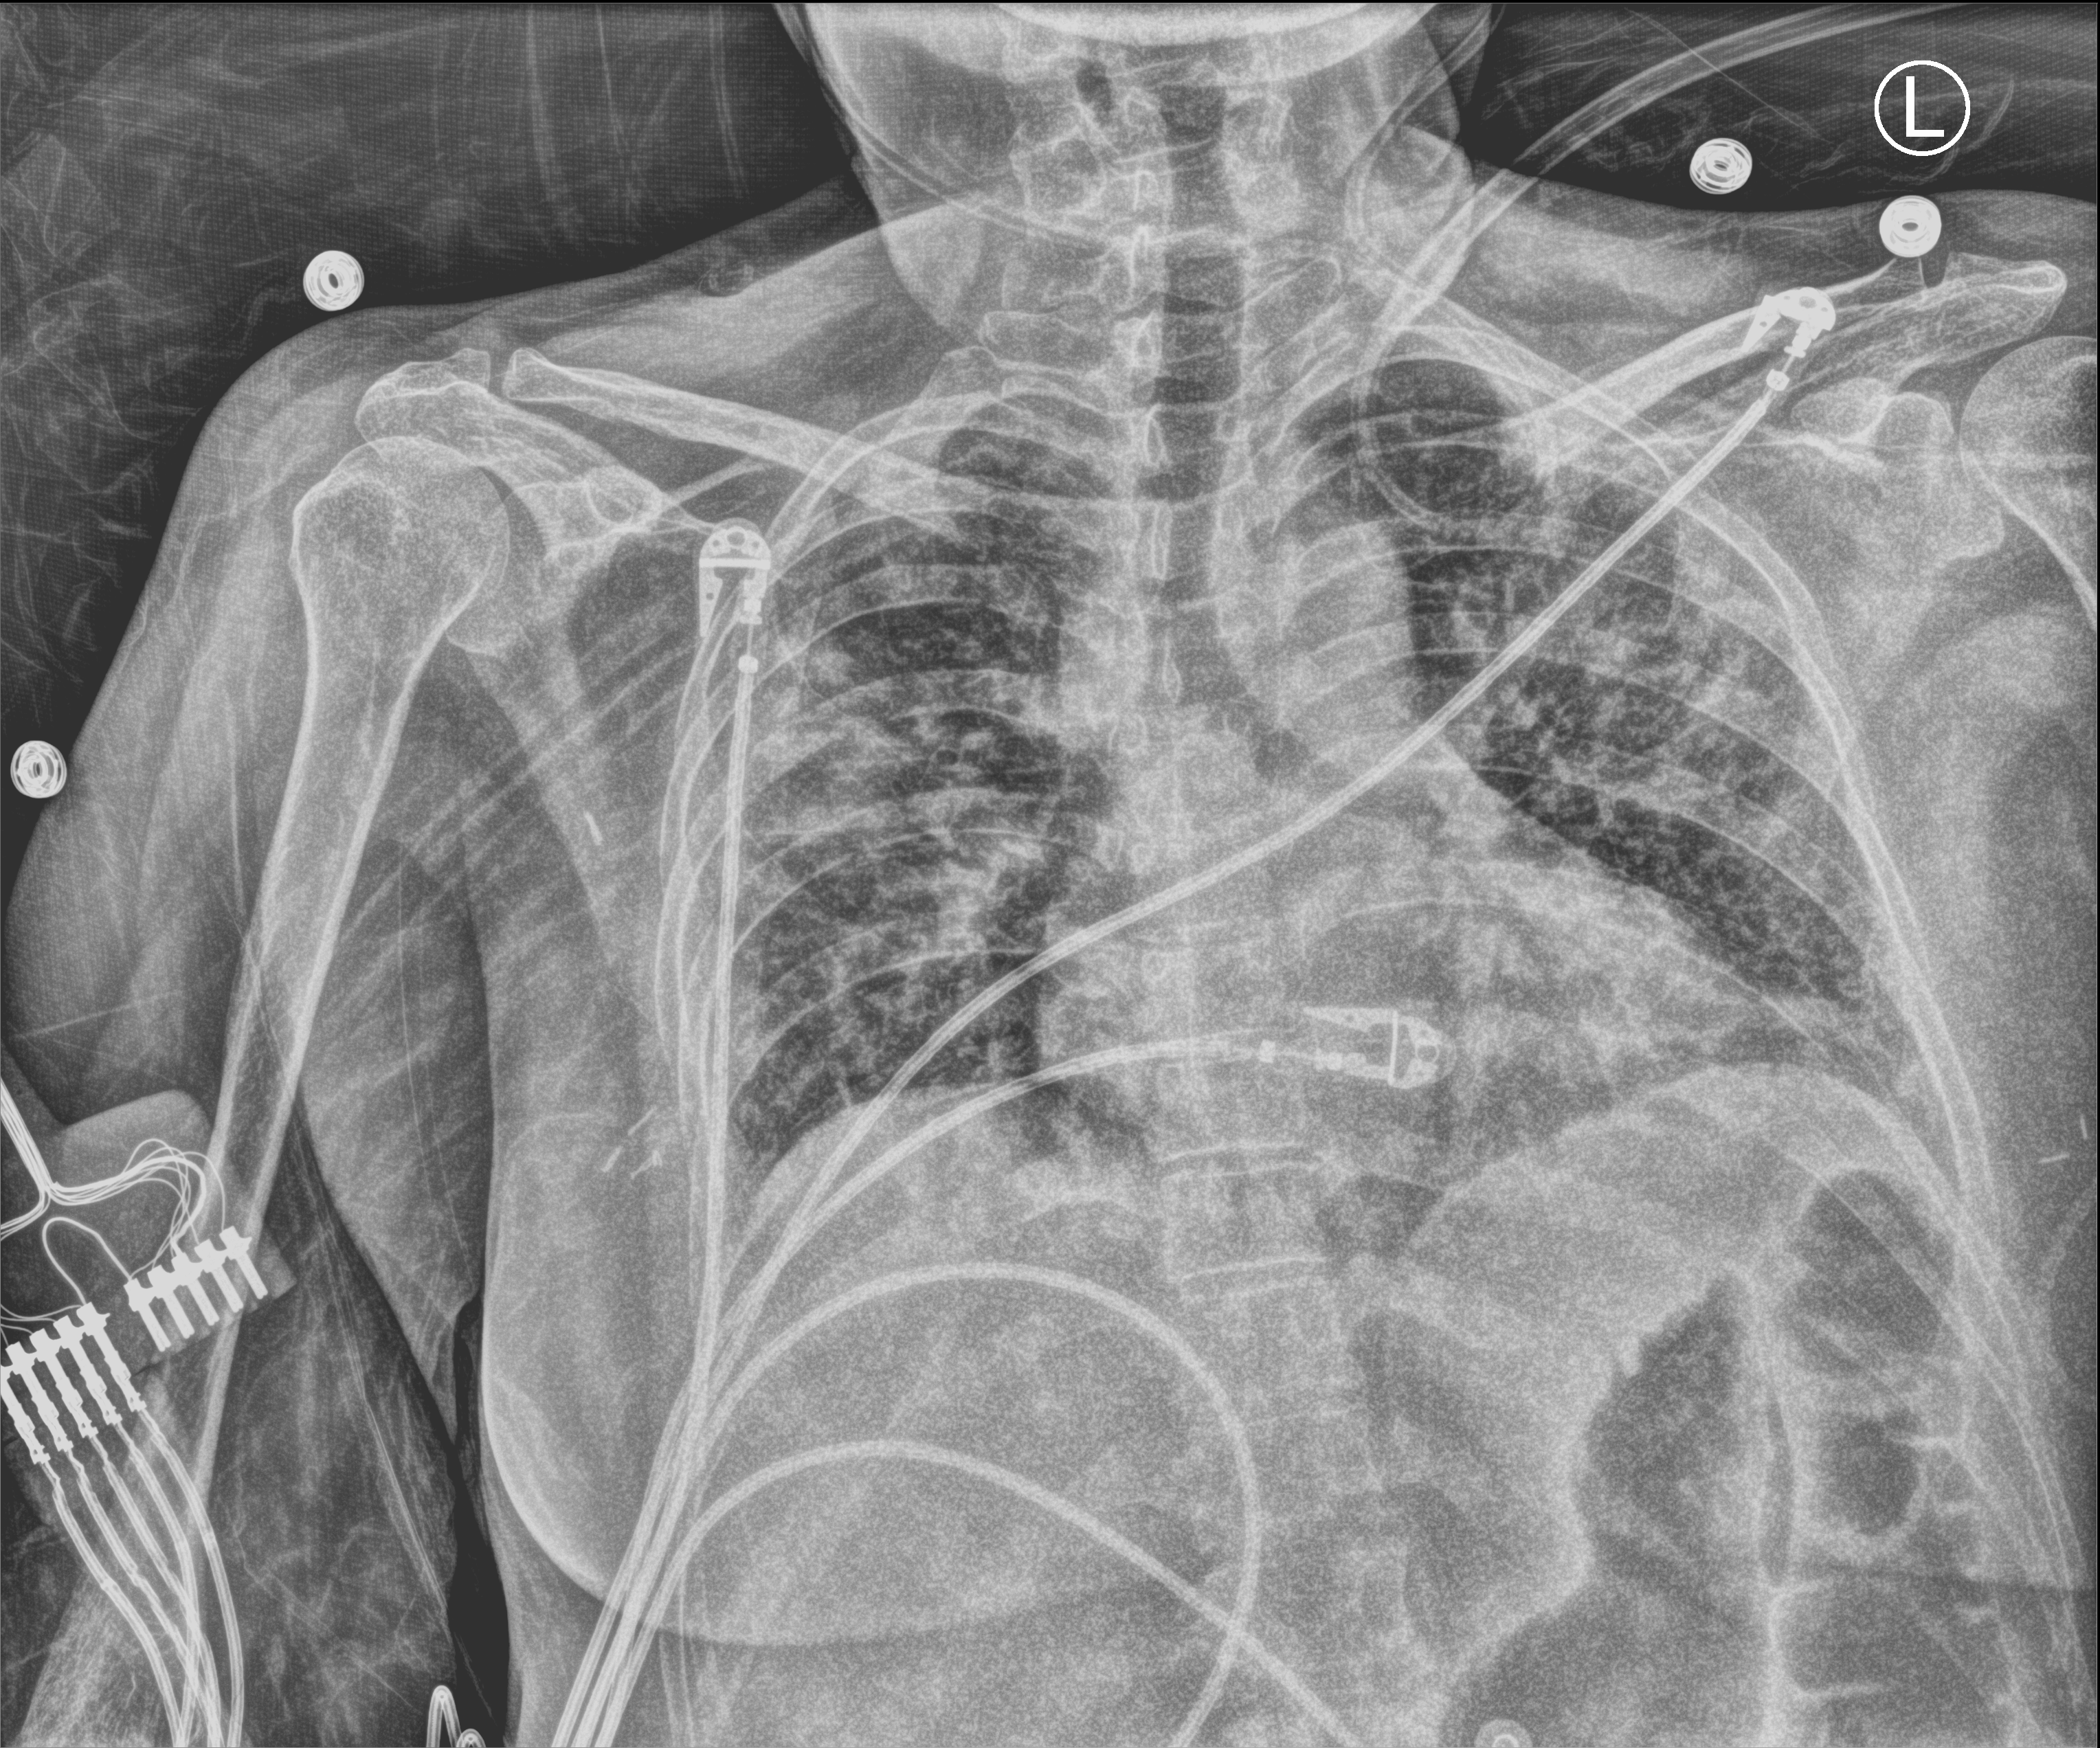
Portable chest radiograph; anteroposterior (AP) projection. Female patient hospitalised with COVID-19, age 18–59 years.
From the hospital-stay record, not from the radiograph (when in the stay this image was taken is not recorded):
- hypertension (admission record): no
- length of hospital stay: 21 days